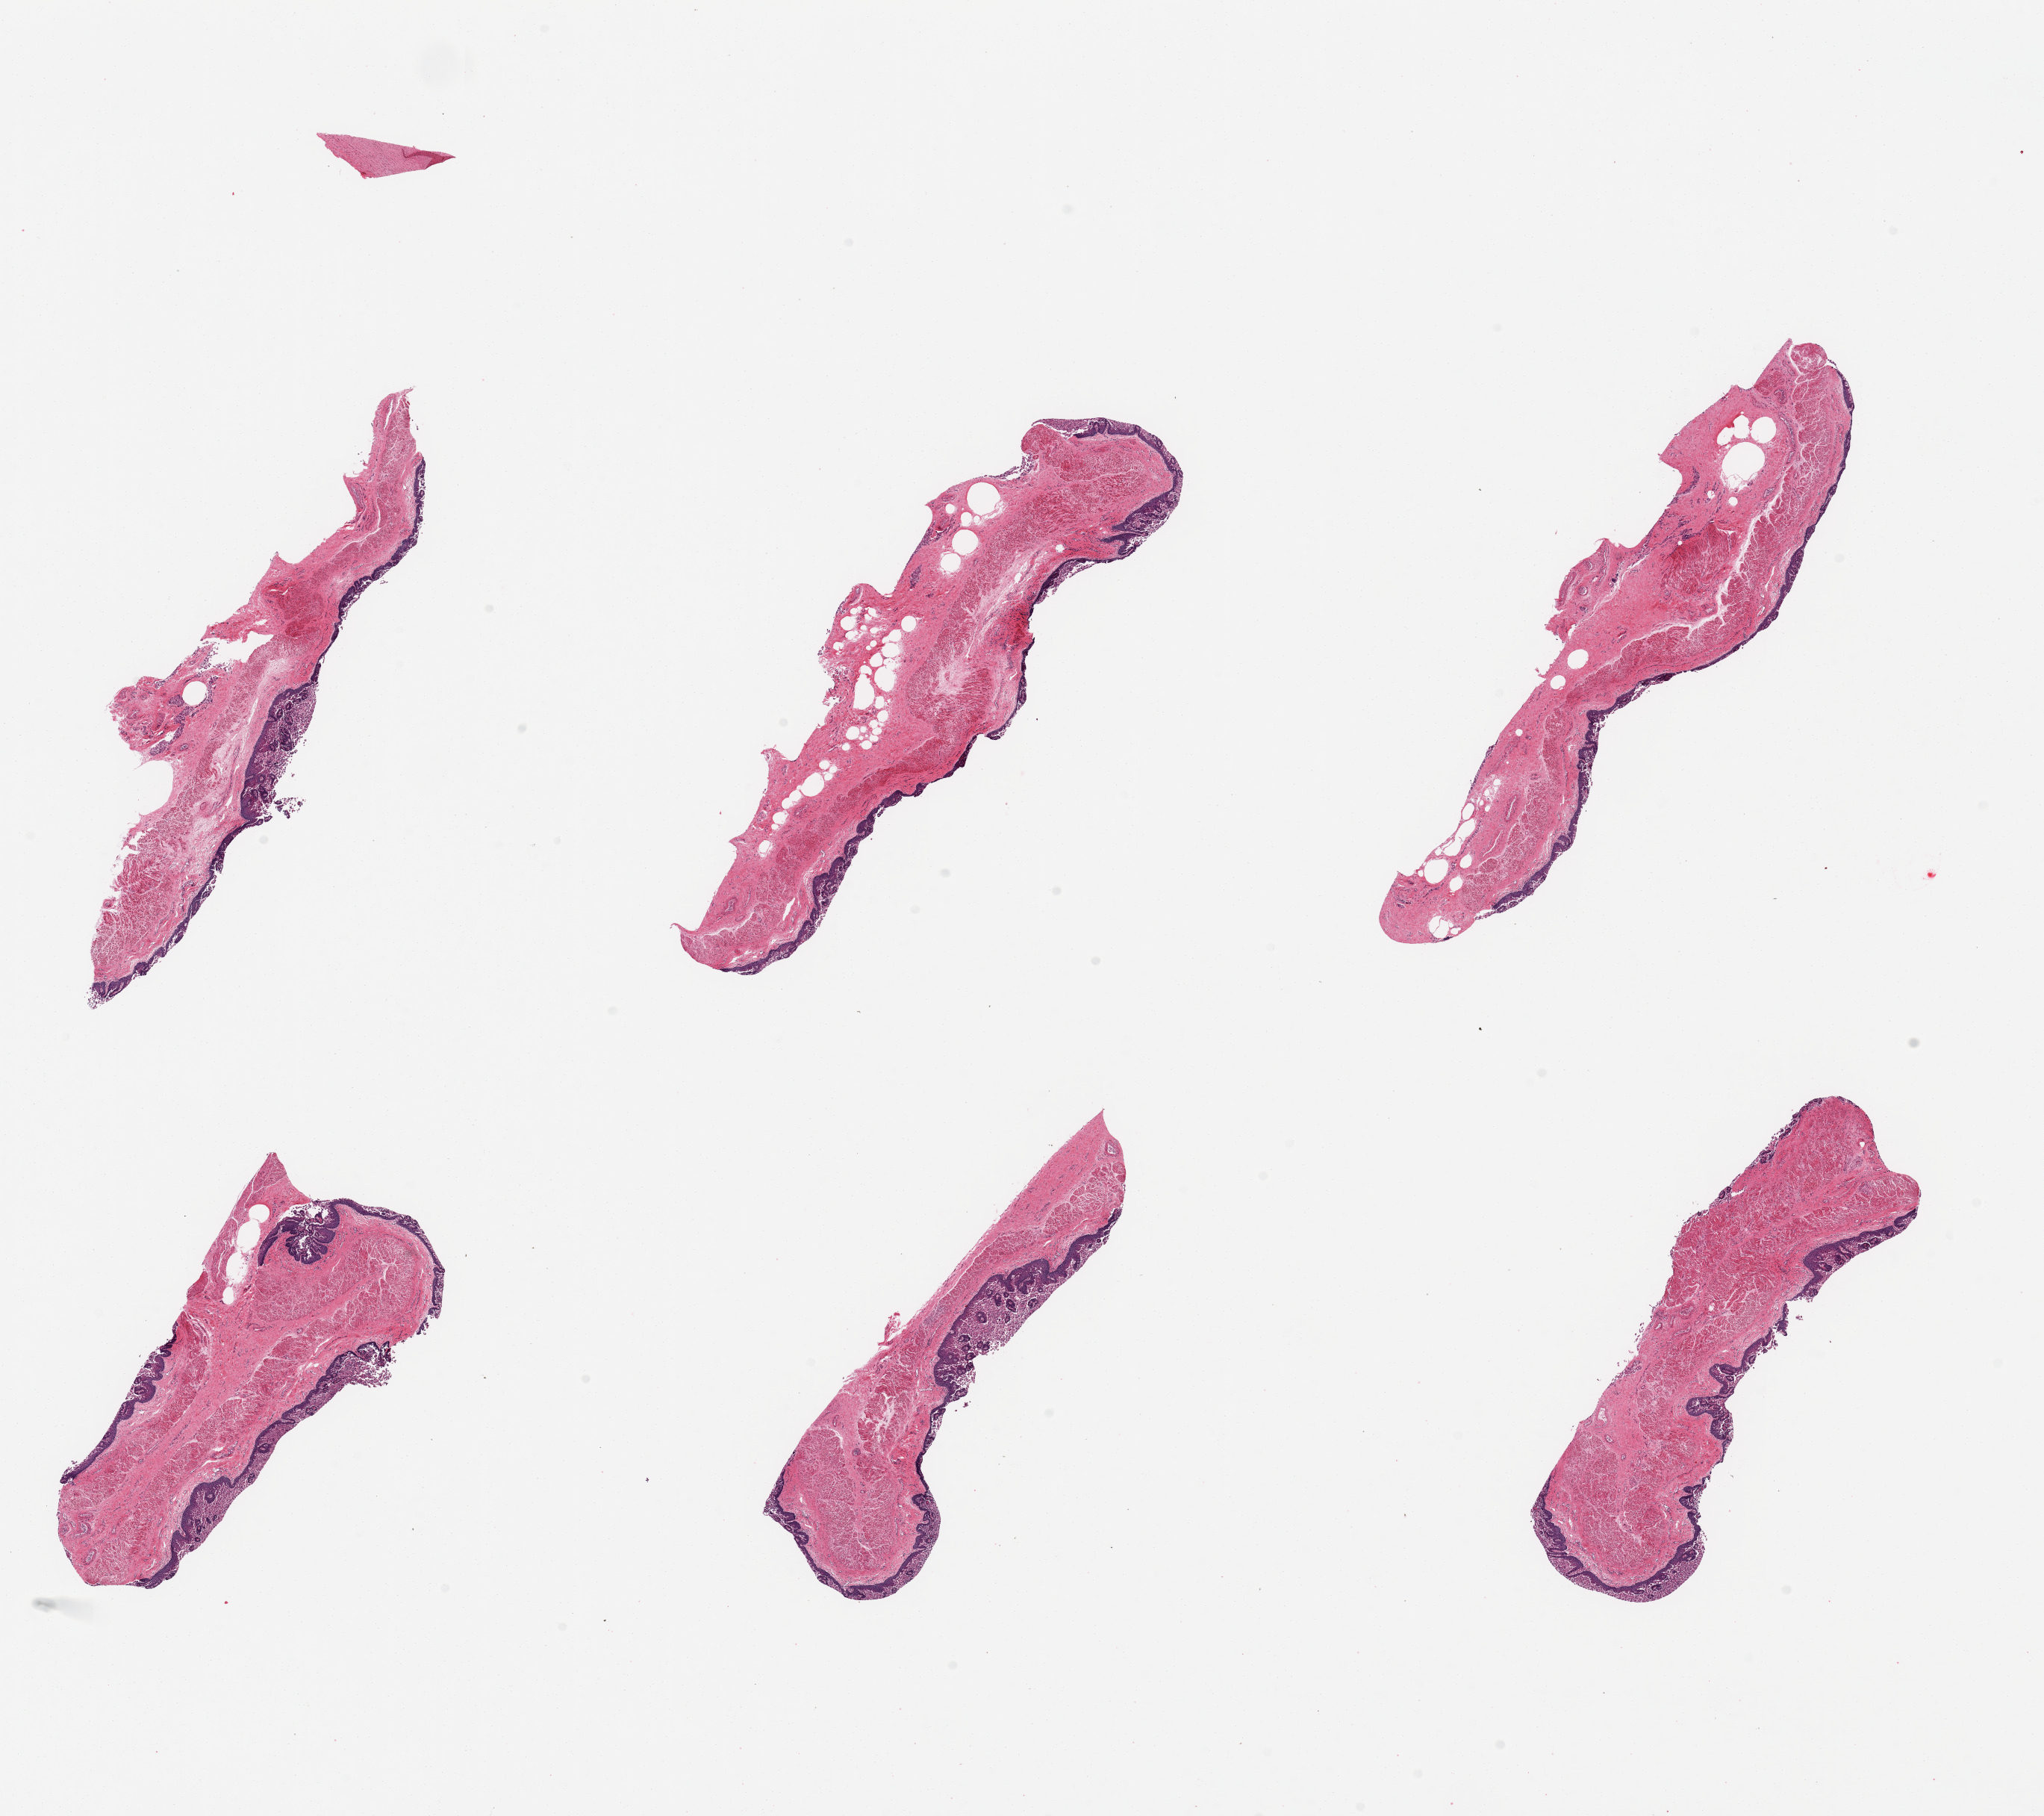
Digitized haematoxylin and eosin-stained section, low-resolution overview of the scanned area, about 21.7 x 19.2 mm (from a 20x scan); PAXgene-fixed, paraffin-embedded tissue; sampled site (target tissue): esophageal mucous membrane; donor tissue sample. Donor: male.
Reviewer comment on this tissue sample: 6 pieces; squamous epithelium partially sloughed.